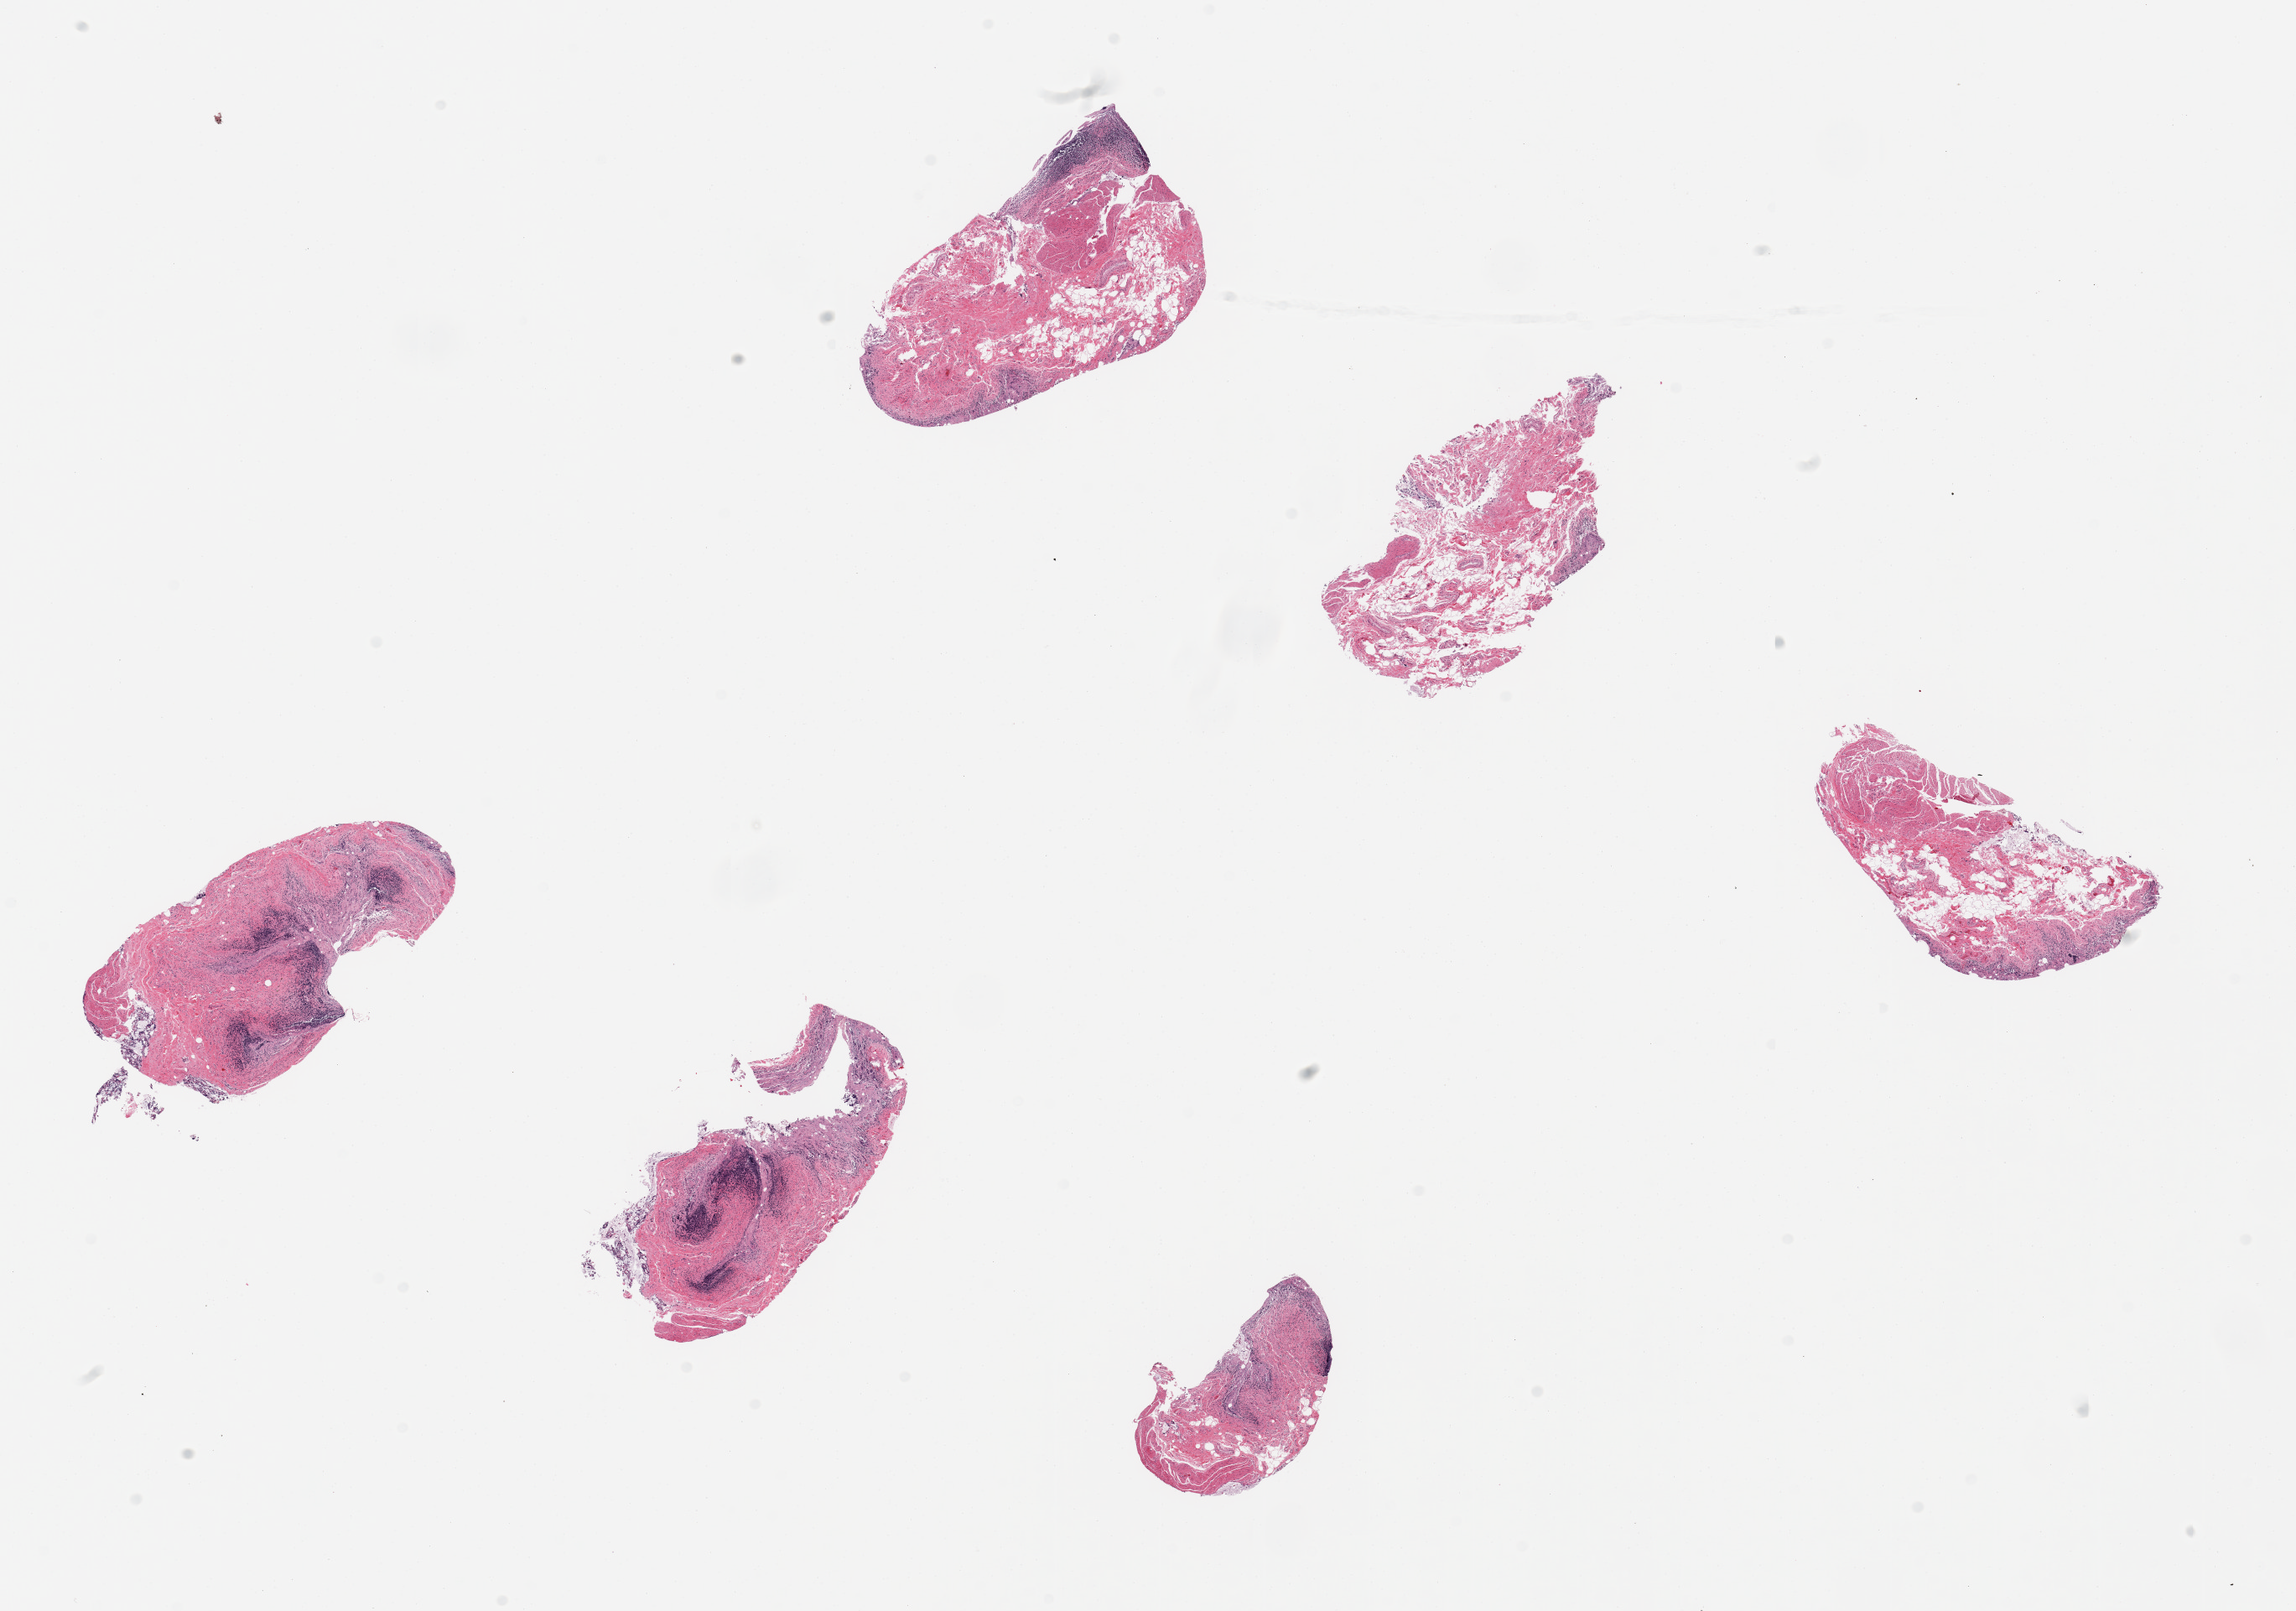
Whole-slide image, H&E stain, low-resolution overview of the scanned area, about 21.7 x 15.2 mm. Female donor.
Specimen: PAXgene-fixed paraffin-embedded (PFPE) section; section of ileum (target tissue); tissue donor sample.